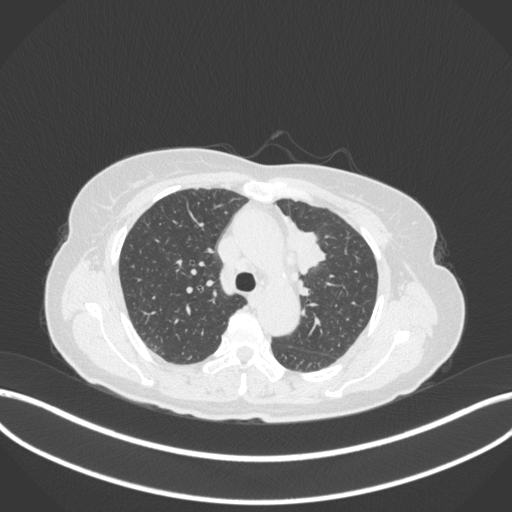
Chest CT, one axial slice; slice 234 of 368 in the series (ordered by position); reconstruction kernel B31f; lung window (W 1500 / L -600 HU); 1 mm slice thickness; 512 × 512 image matrix, field of view 400 × 400 mm. Female patient, age 65 years. From the clinical record (not read from this slice): clinical TNM (as recorded): T2a N0 M0; histopathological grade: G2-3.
Annotated regions visible in this slice (rectangle marked by the reading radiologist):
- lung tumour (recorded histology: adenocarcinoma): bounding box <276,206,327,276> (left, top, right, bottom; pixels)